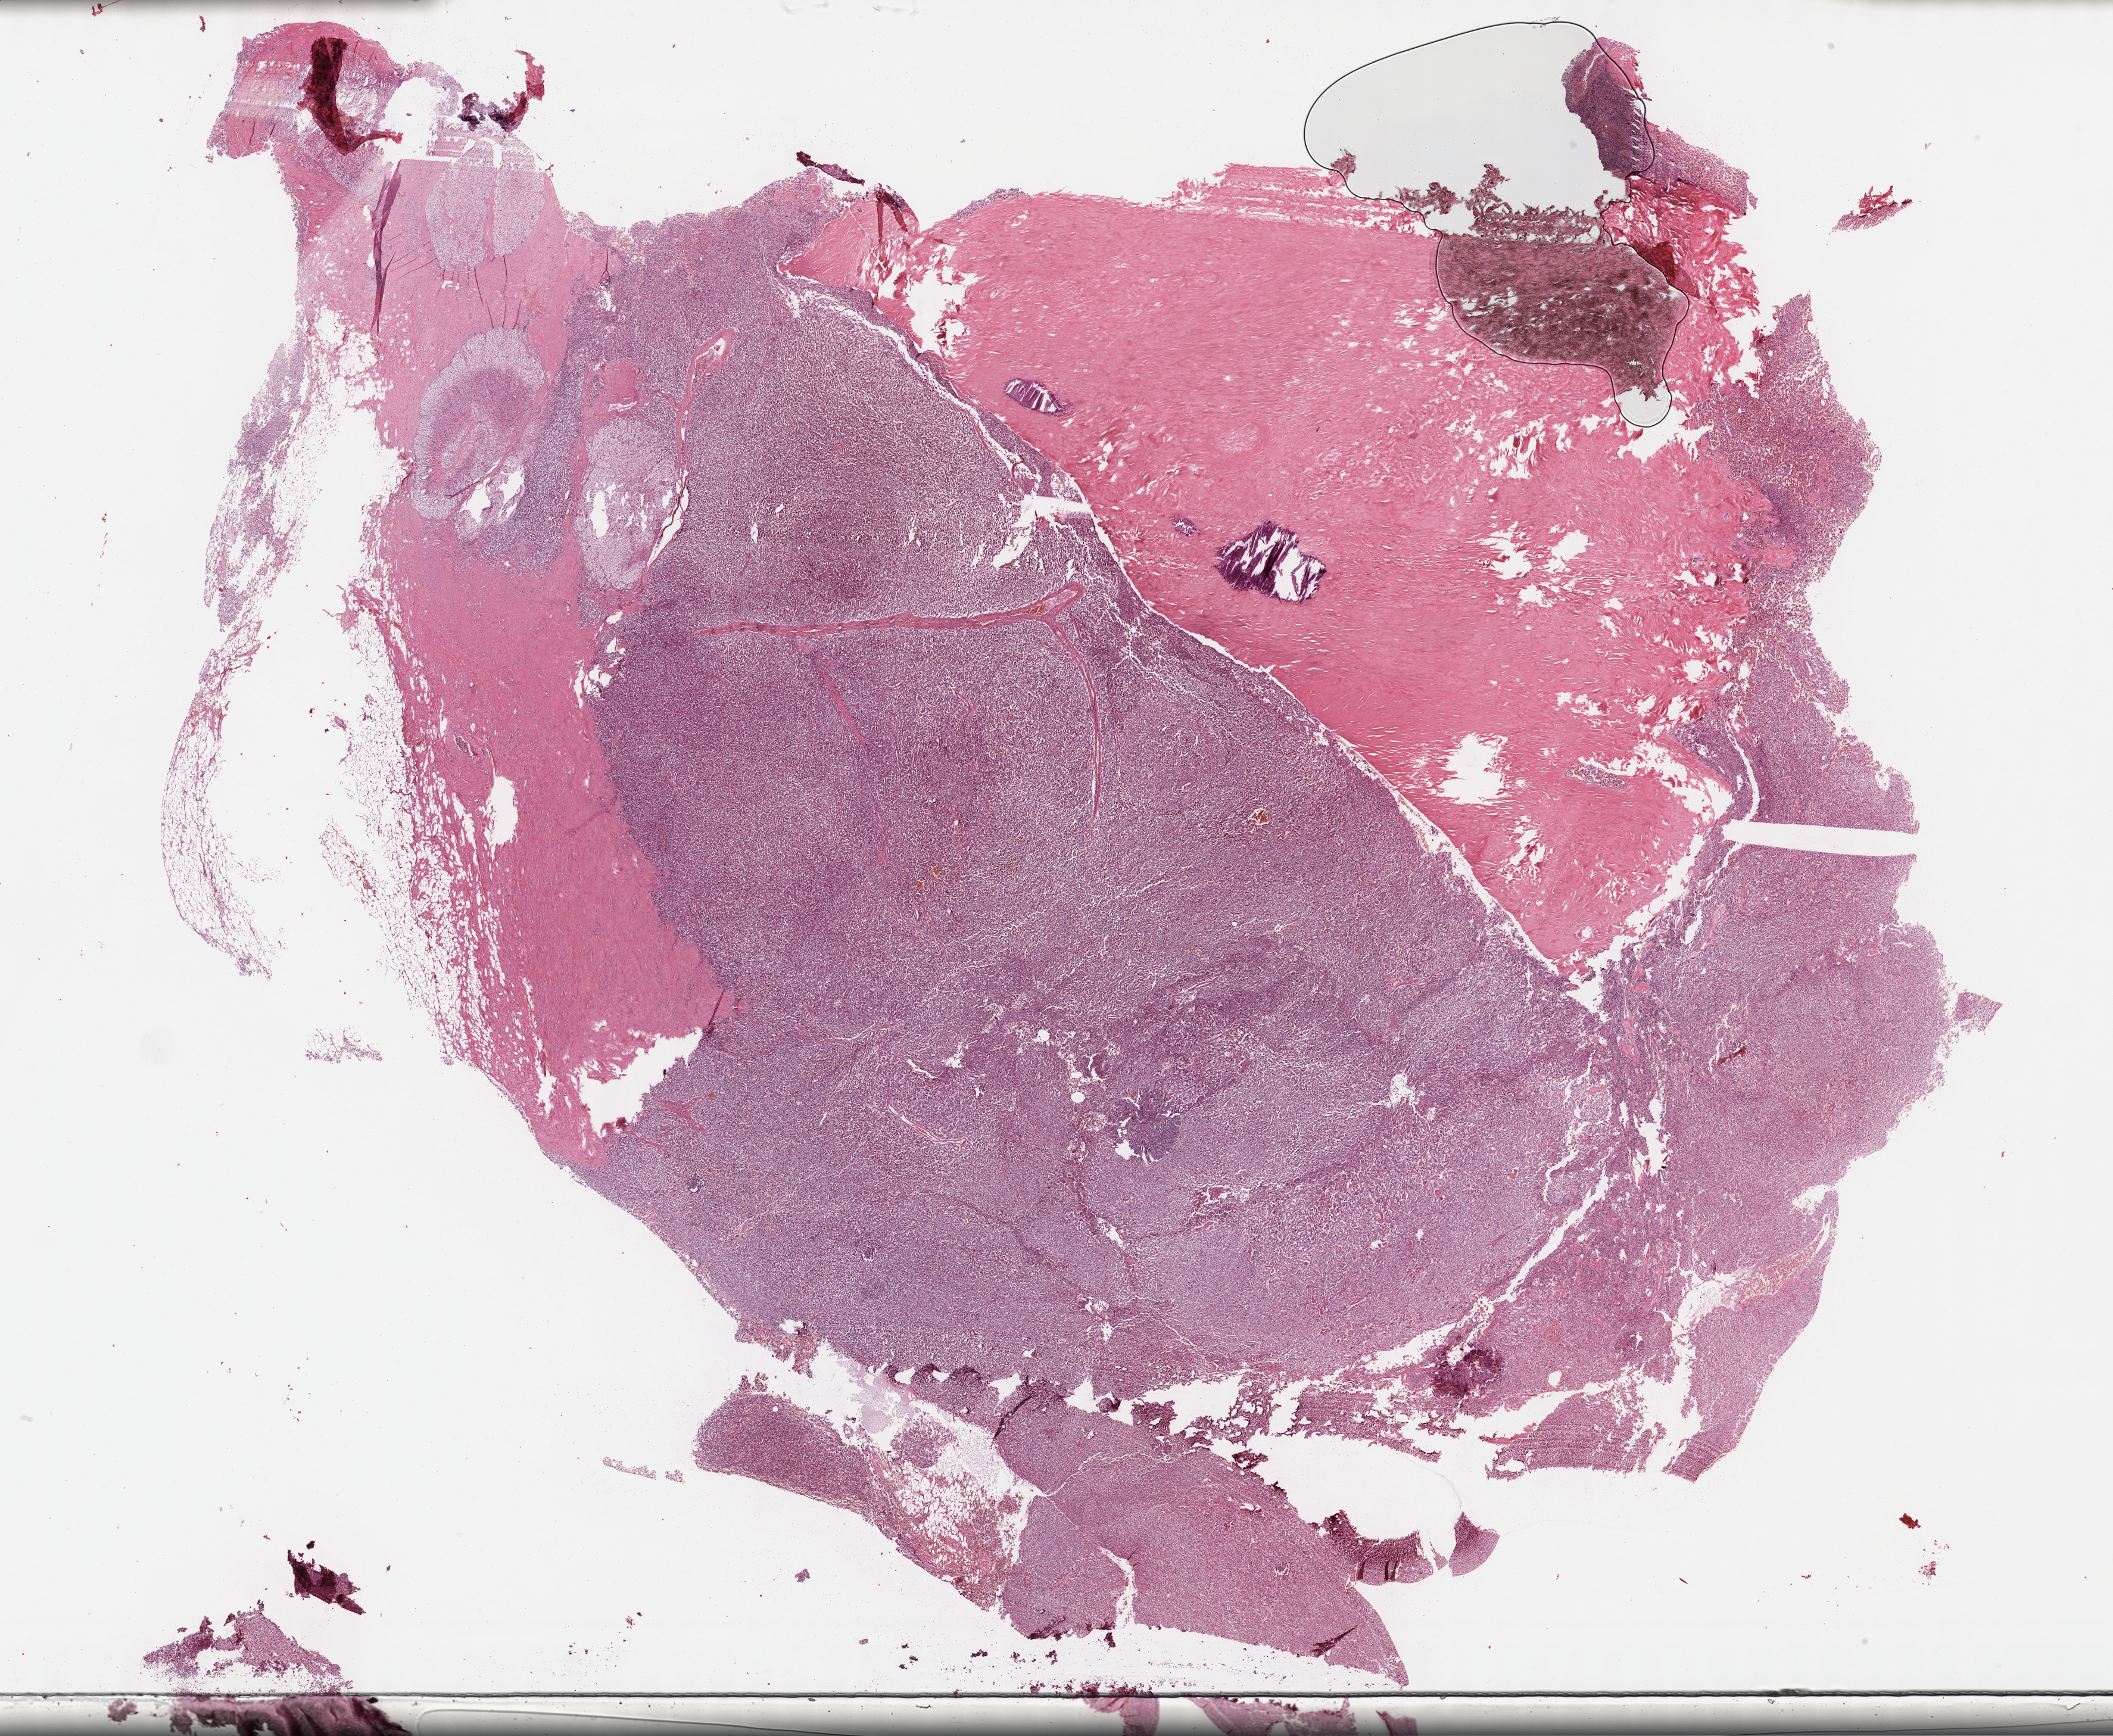
Whole-slide histology image, H&E — a low-resolution overview of the entire scanned area, about 28.7 x 23.6 mm; FFPE section; adrenal gland, primary tumour sample. Male patient; age at initial diagnosis 74 years.
* pathologic diagnosis: Pheochromocytoma, malignant